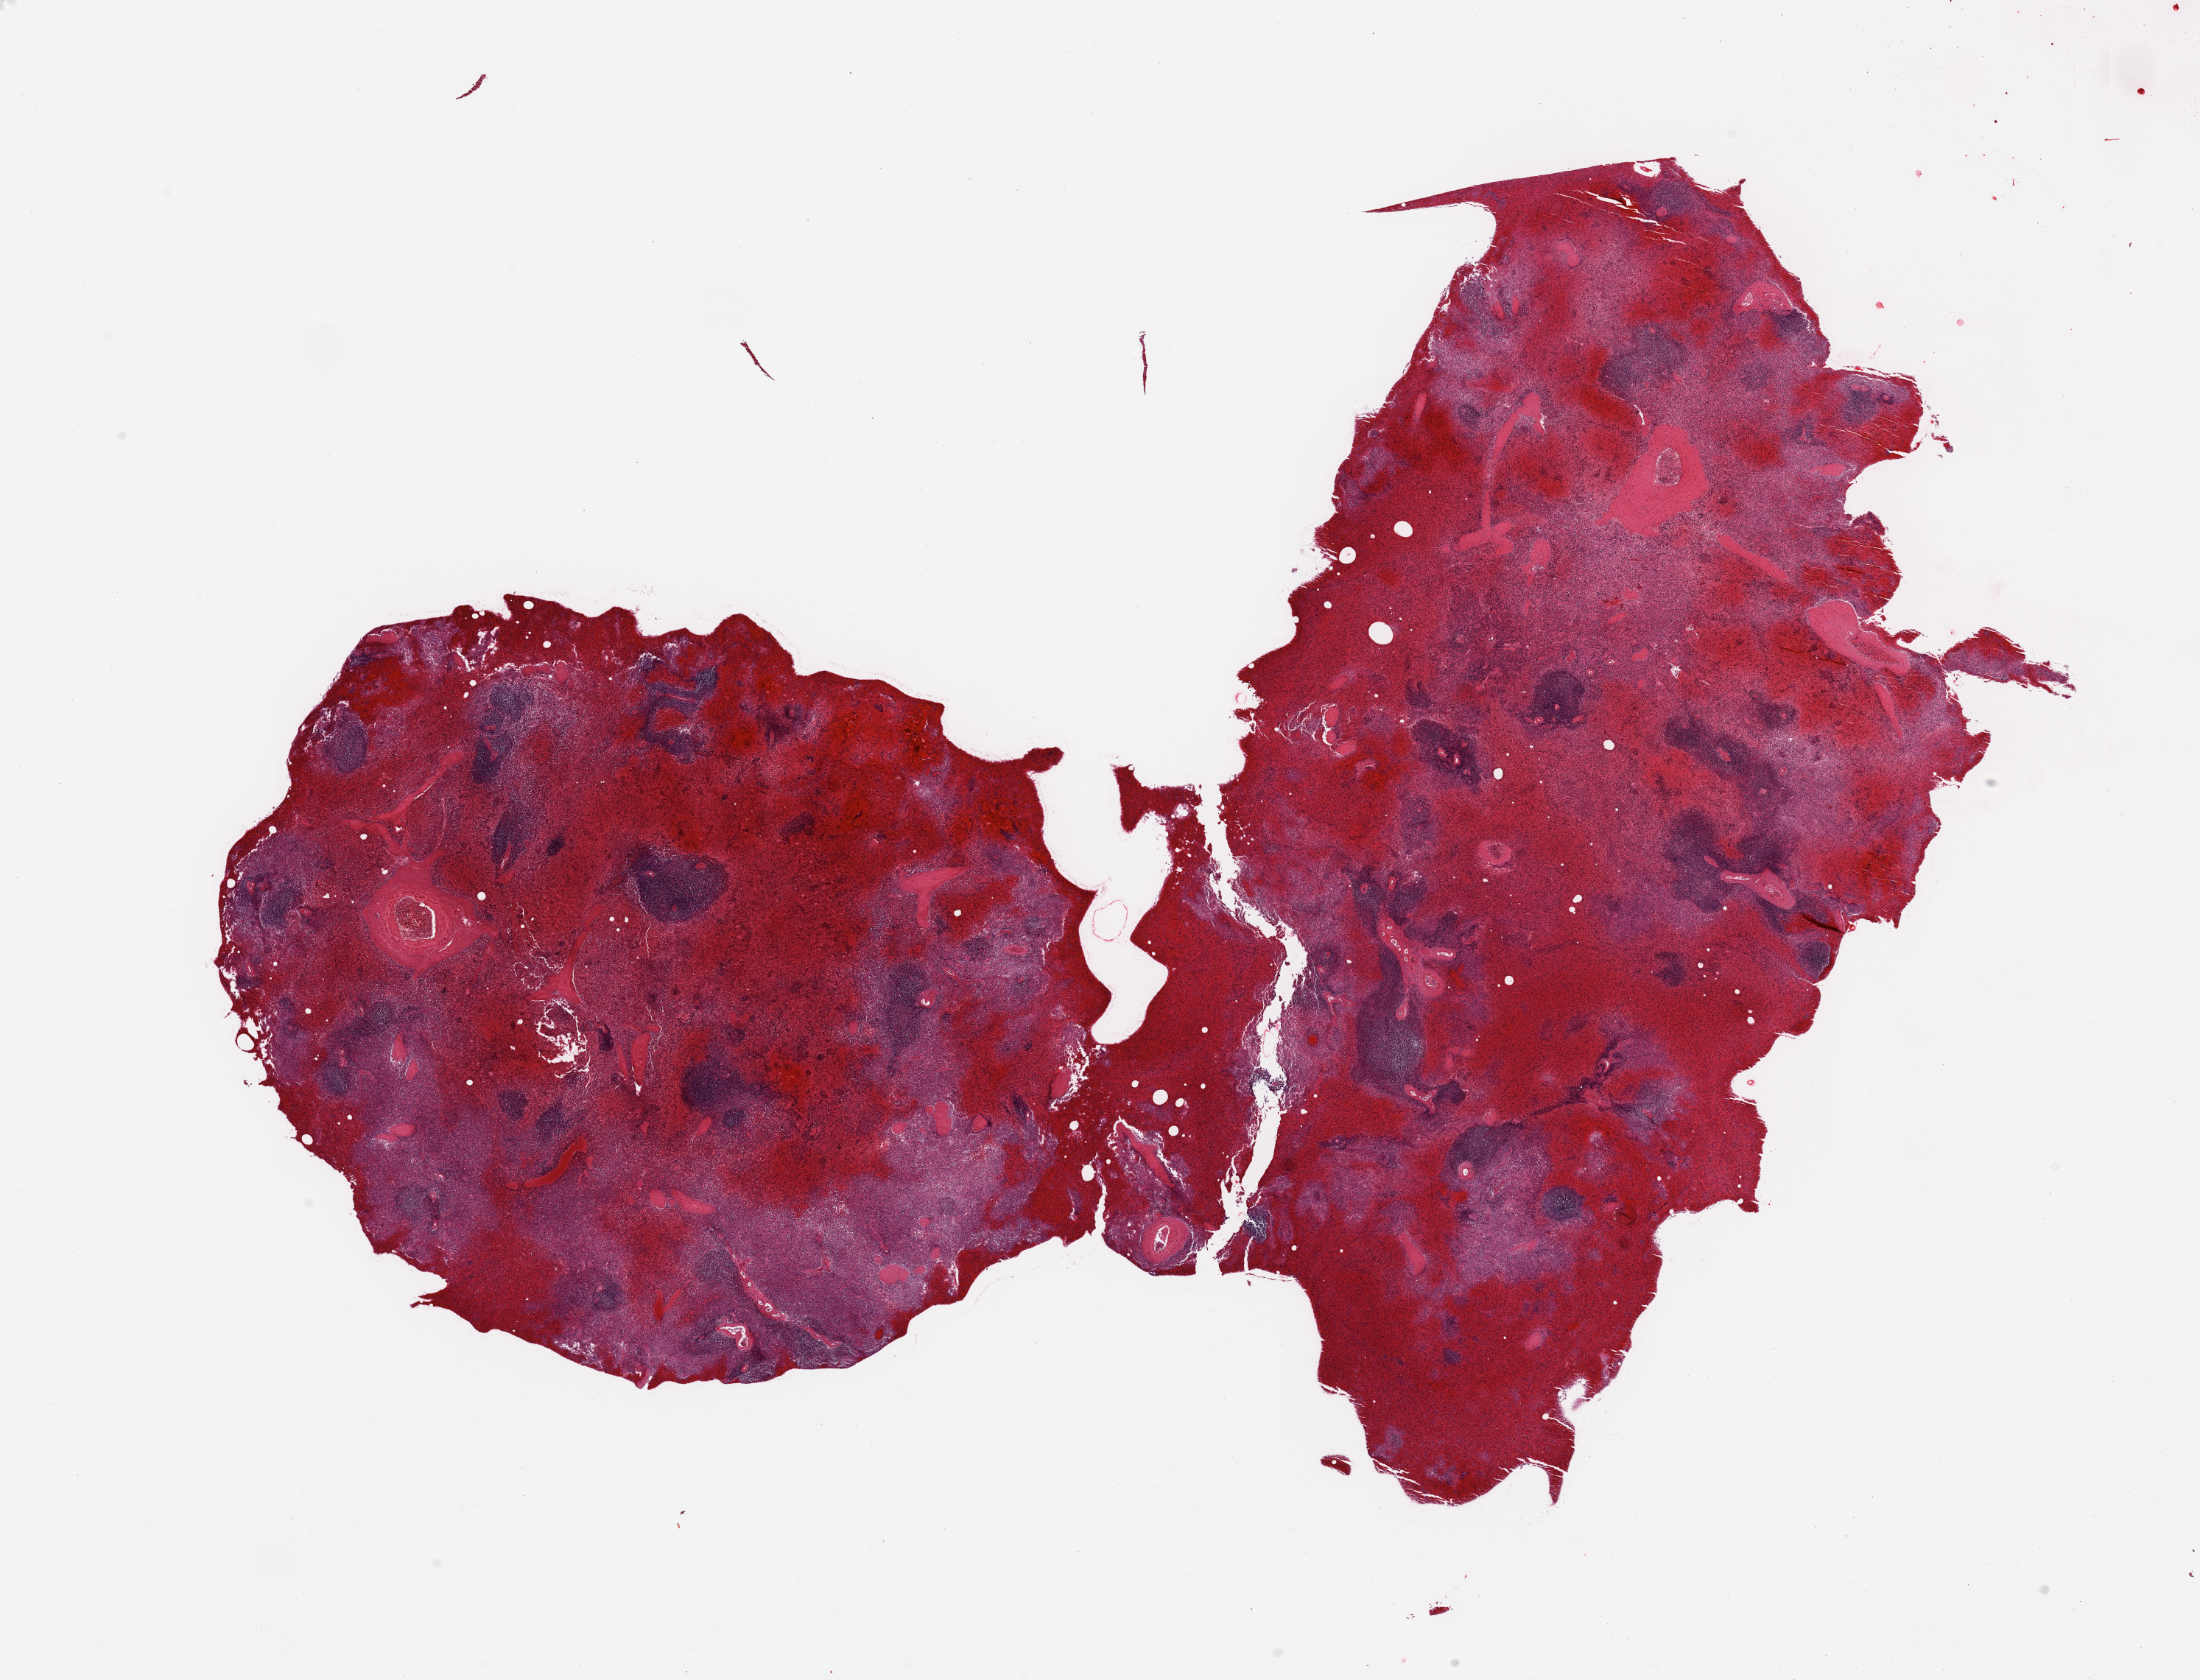
Digitized hematoxylin and eosin (H&E)-stained section, whole scanned area (about 23.6 x 18.0 mm, from a 20x scan) shown as a low-resolution overview; PAXgene-fixed, paraffin-embedded tissue; target tissue: spleen; donor tissue sample. Donor sex: male.
* pathologist's review note for this sample: 2 pieces; severe congestion